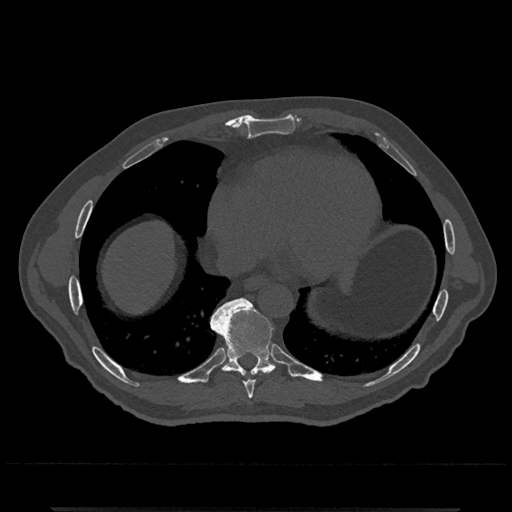
CT including the spine, one axial slice. Slice 634 of 797 in the series (ordered by position). 120 kVp. Bone window (W 1800 / L 400 HU). 0.5 mm slice thickness. 512 × 512 image matrix, field of view 393 × 393 mm. Patient: male, 67 years. Case-level facts recorded for this patient, not image findings: primary cancer: prostate.
Annotated regions visible in this slice (semi-automatic segmentation, software-assisted and operator-edited):
- T8 vertebra: box from (x=244, y=380) to (x=255, y=399) px
- T9 vertebra: (x=211, y=298)–(x=278, y=378)